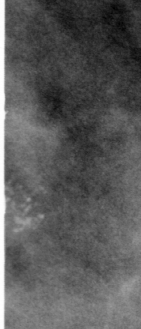
Crop from a digitized film mammogram around one marked abnormality, left breast, CC view.
- Marked abnormality: calcifications, morphology pleomorphic, distribution clustered; BI-RADS assessment category 4; subtlety rating 5 on a 1 (subtle) to 5 (obvious) scale; pathology result (as recorded, not read from the image): benign.